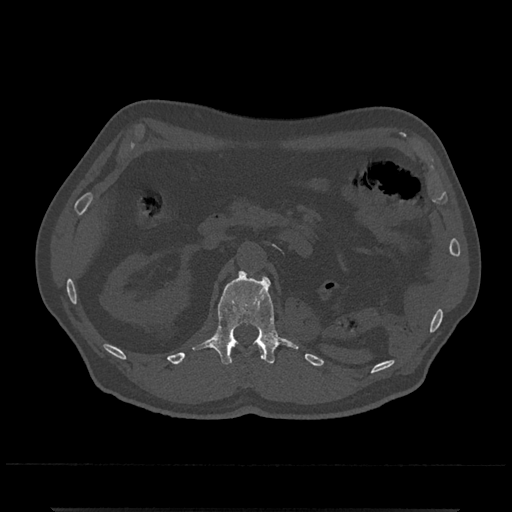
CT including the spine, one axial slice. Slice 372 of 797 in the series (ordered by position). 120 kVp. Bone window (W 1800 / L 400 HU). 512 × 512 image matrix, field of view 393 × 393 mm. Male patient, age 67 years. Case-level facts recorded for this patient, not image findings: primary cancer: prostate.
Outlined on this slice (semi-automatically segmented with operator editing):
- L1 vertebra: box from (x=192, y=269) to (x=300, y=365) px
- T12 vertebra: (x=257, y=343)–(x=265, y=358)